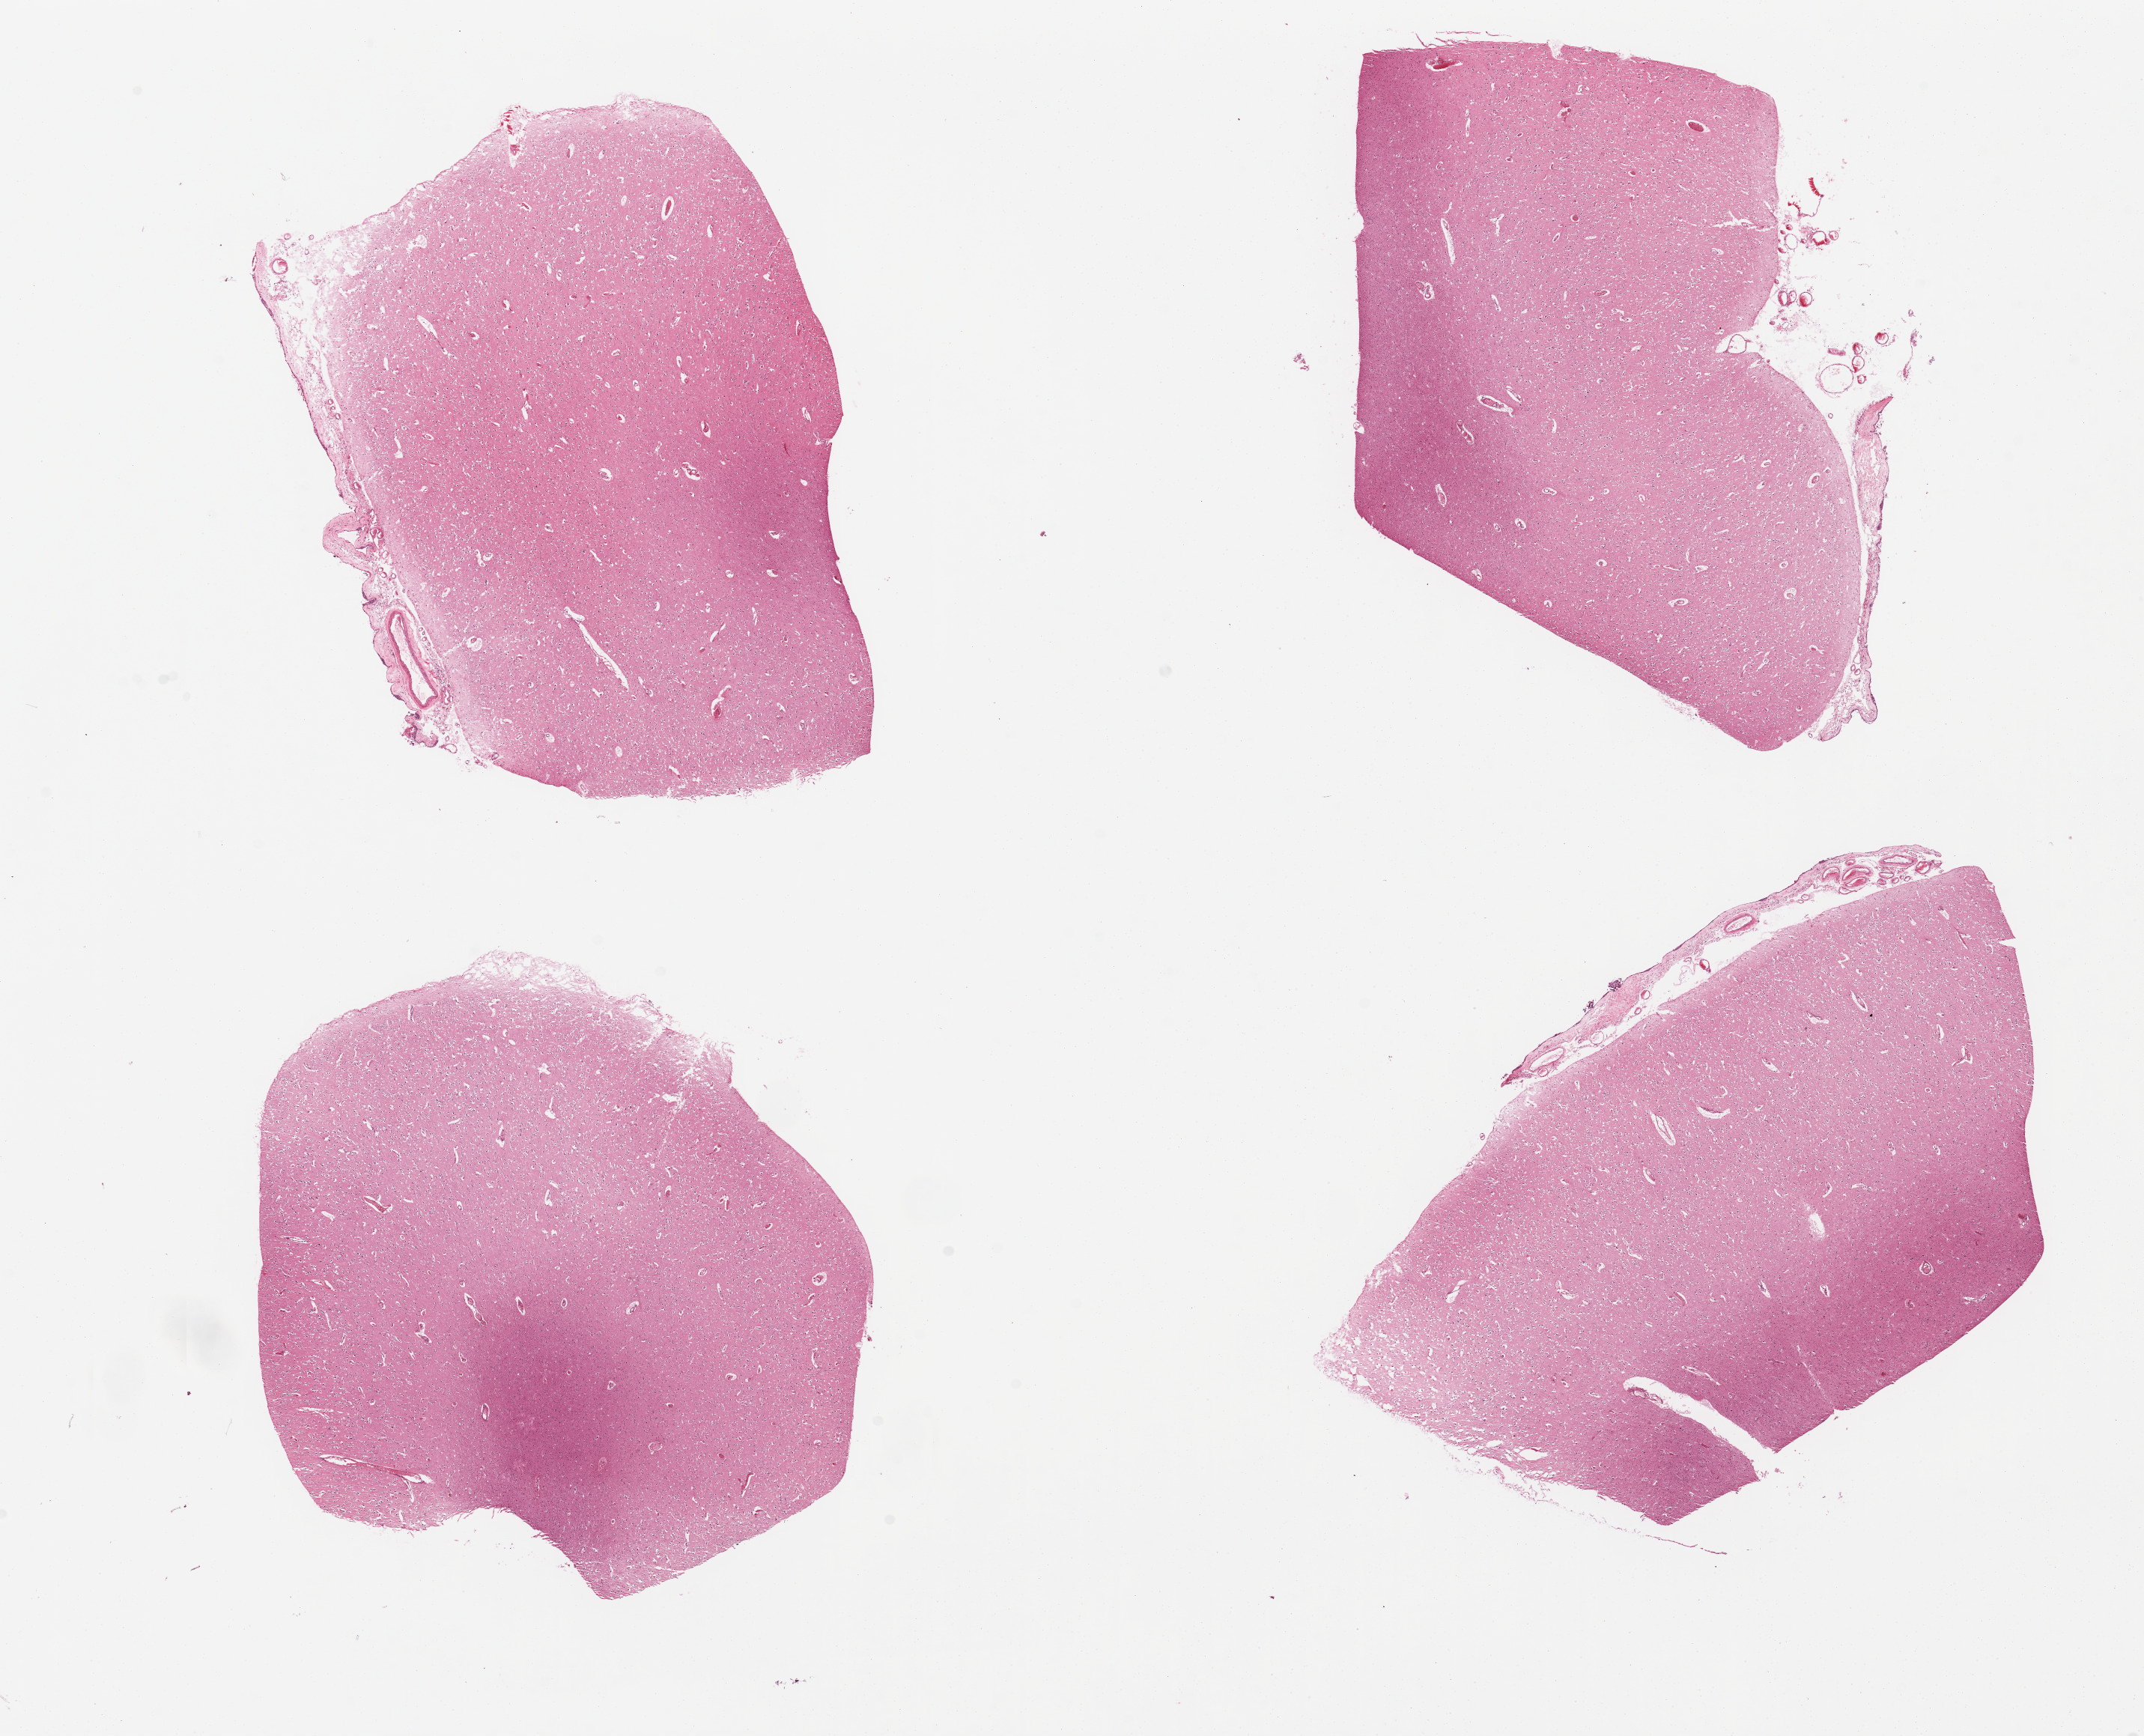
Digitized haematoxylin and eosin-stained section — a low-resolution overview of the entire scanned area, about 22.6 x 18.3 mm, PAXgene-fixed, paraffin-embedded tissue, sampled site (target tissue): cerebral cortex, tissue donor sample.
Reviewer comment on this tissue sample: 4 pieces, appears edematous.